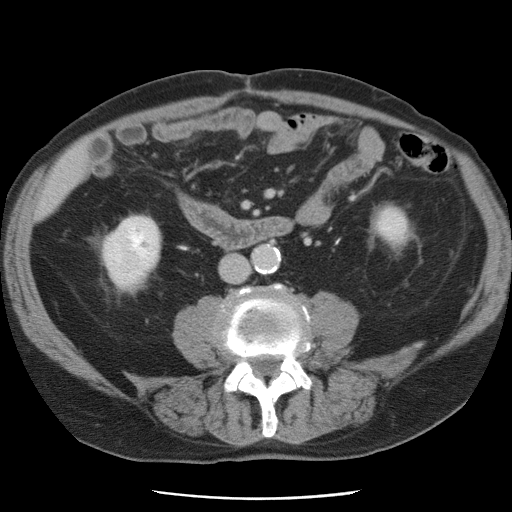
Contrast-enhanced abdominal CT, one axial slice. Slice 12 of 78 in the series (ordered by position). 120 kVp. Intravenous contrast given. Soft-tissue window (W 400 / L 40 HU). 5 mm slice thickness. 512 × 512 image matrix, field of view 337 × 337 mm. Male patient, age 75 years. From the clinical record (not read from this slice): diagnosis: colorectal cancer liver metastases, imaged before liver resection.
Outlined on this slice (manually delineated by an expert):
- liver: bounding box [x1, y1, x2, y2] px = [39, 148, 86, 216]
- planned liver remnant (the part of the liver to remain after resection): [39, 148, 87, 216]